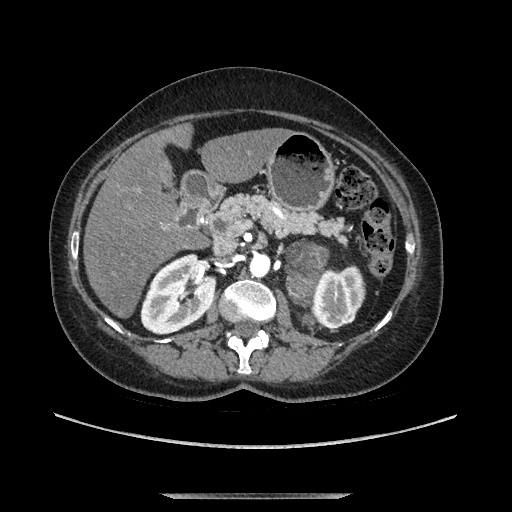
Contrast-enhanced abdominal CT, one axial slice; soft-tissue window (W 400 / L 40 HU); 1.25 mm slice thickness; 512 × 512 image matrix. Female patient. From the clinical record (not read from this slice): diagnosis: adrenocortical carcinoma; tumour side: left adrenal; tumour size at pathology: 9 cm; Ki-67 index: 2 %; stage (as recorded): 3.
Annotated regions visible in this slice (semi-automatic segmentation, software-assisted and operator-edited):
- mass: bounding box [x1, y1, x2, y2] px = [288, 246, 322, 298]